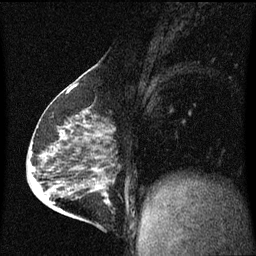
Breast MRI (dynamic contrast-enhanced), one sagittal slice; slice 27 of 60 in the series (ordered by position); dynamic contrast-enhanced series, image 2 of 3 at this slice position (ordered by acquisition); 1.5 T; TE 4.2 ms, TR 8 ms; 2 mm slice thickness; 256 × 256 image matrix. Female patient, age 63 years.
Outlined on this slice (semi-automatically segmented with operator editing):
- analysis volume of interest (the breast-tissue region the enhancement analysis was run in; not a lesion): bounding box [x1, y1, x2, y2] px = [88, 182, 117, 229]
- tumour enhancement mask (voxels above the 70 % enhancement threshold inside the analysis volume of interest): [90, 190, 109, 203]